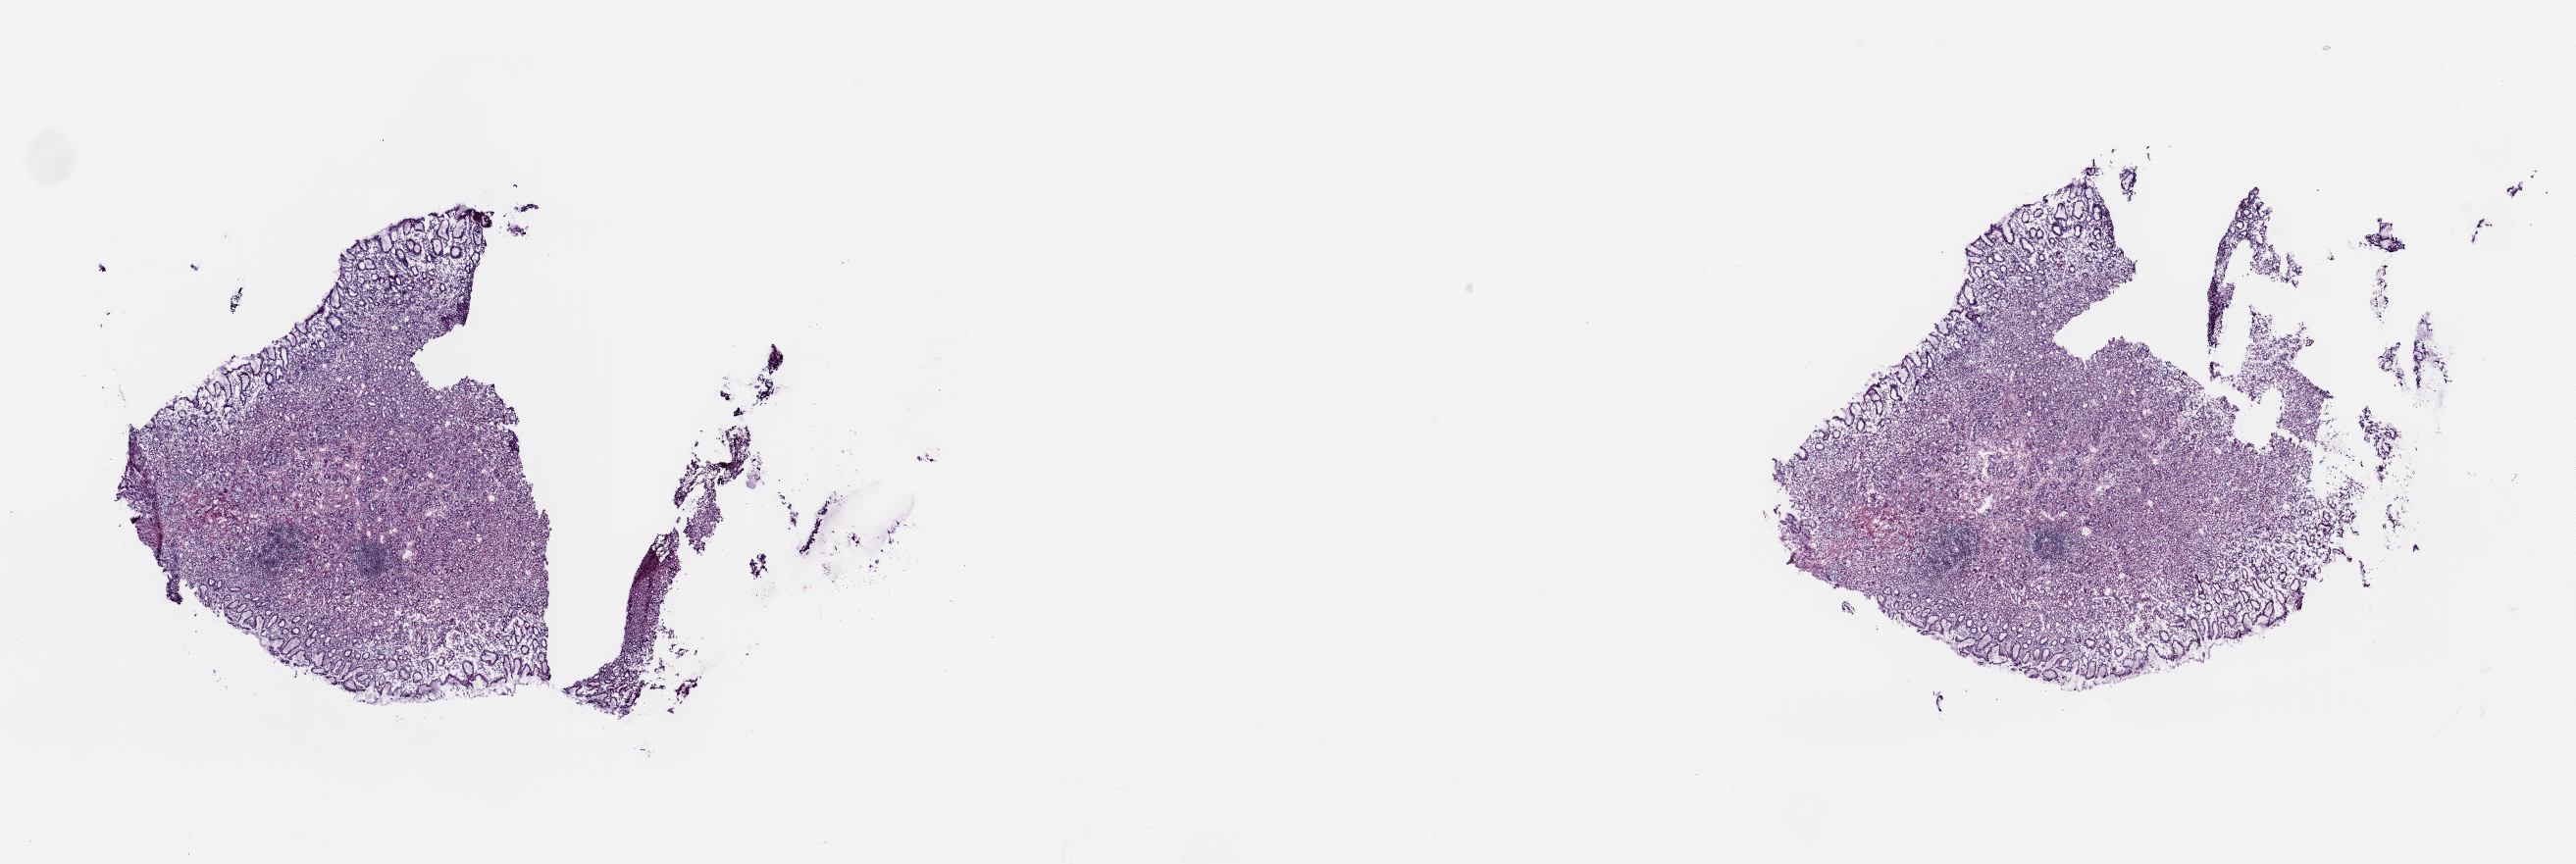
Whole-slide histology image, H&E — low-resolution overview of the scanned area, about 20.8 x 7.0 mm (acquisition: 20x scan), frozen section from the top of the tissue portion, esophagus, solid tissue normal (non-tumour tissue) sample. Male patient; age at initial diagnosis 70 years. Composition of this section per pathologist review: tumour cells 0%, tumour nuclei 0%, normal cells 65%, stromal cells 35%, necrosis 0%. Inflammatory infiltration, as recorded: lymphocyte infiltration 20%, monocyte infiltration 1%, neutrophil infiltration 1%.
This section: solid tissue normal sample (biorepository sample class). Patient diagnosis: Adenocarcinoma, NOS (lower third of esophagus).